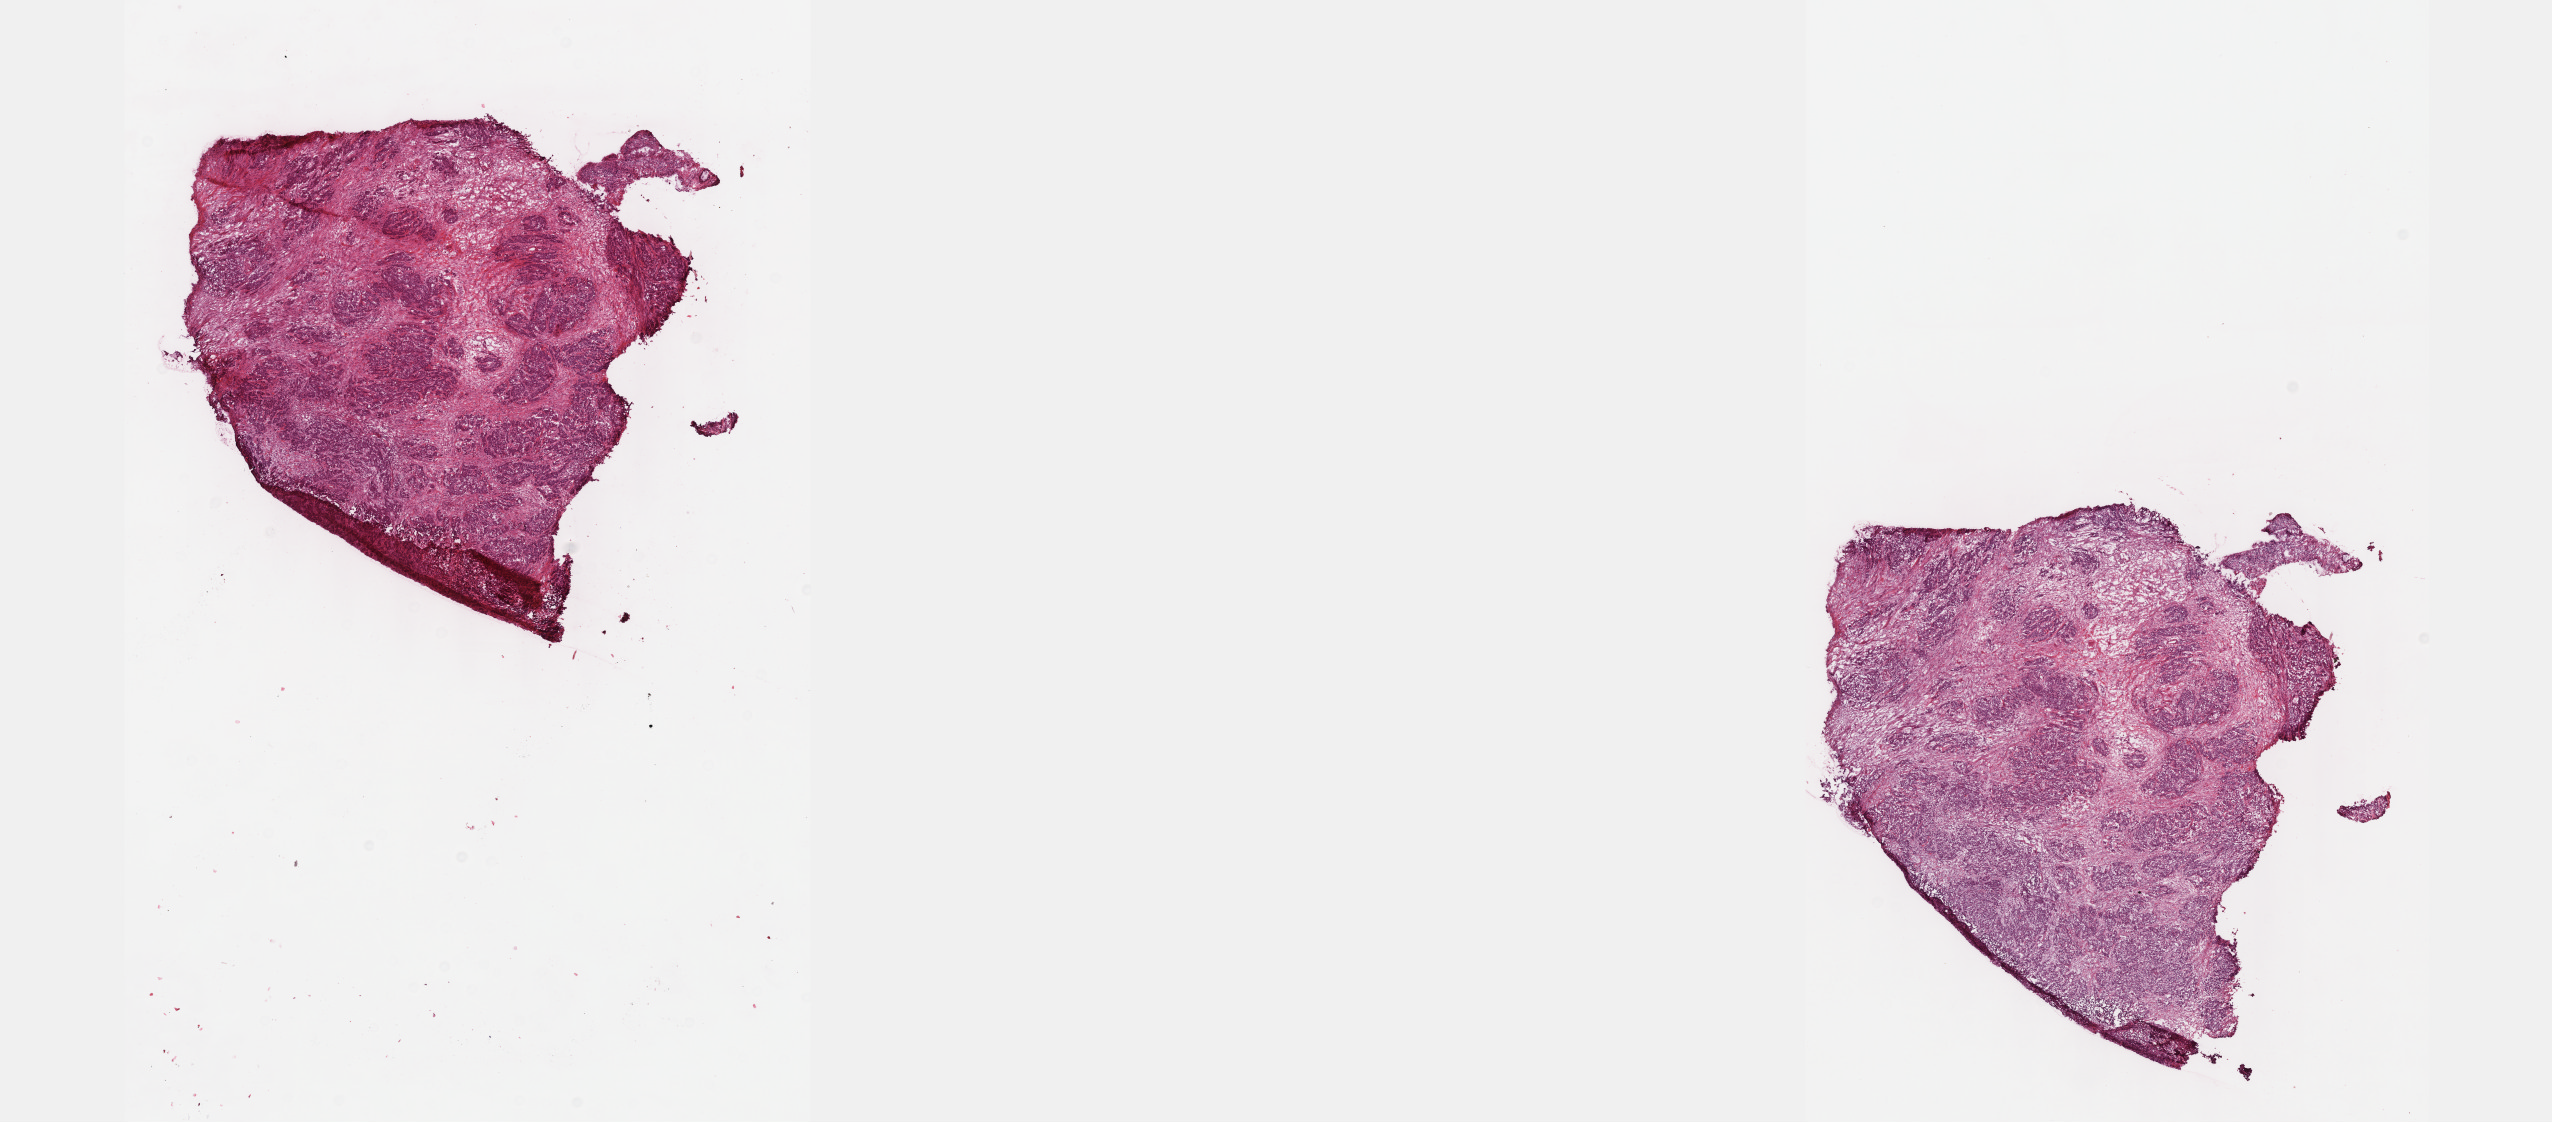
Hematoxylin and eosin (H&E) stained whole-slide image — a low-resolution overview of the entire scanned area, about 20.6 x 9.1 mm (slide scanned at 40x); frozen section from the top of the tissue portion; primary tumour sample from the colon. Female, age 84 years at initial diagnosis. Composition of this section per pathologist review: tumour cells 60%, tumour nuclei 80%, normal cells 0%, stromal cells 30%, necrosis 10%. Inflammatory infiltration, as recorded: lymphocyte infiltration 5%, monocyte infiltration 0%, neutrophil infiltration 5%.
AJCC pathologic stage: IIA (6th edition). Histologic diagnosis: Adenocarcinoma, NOS.